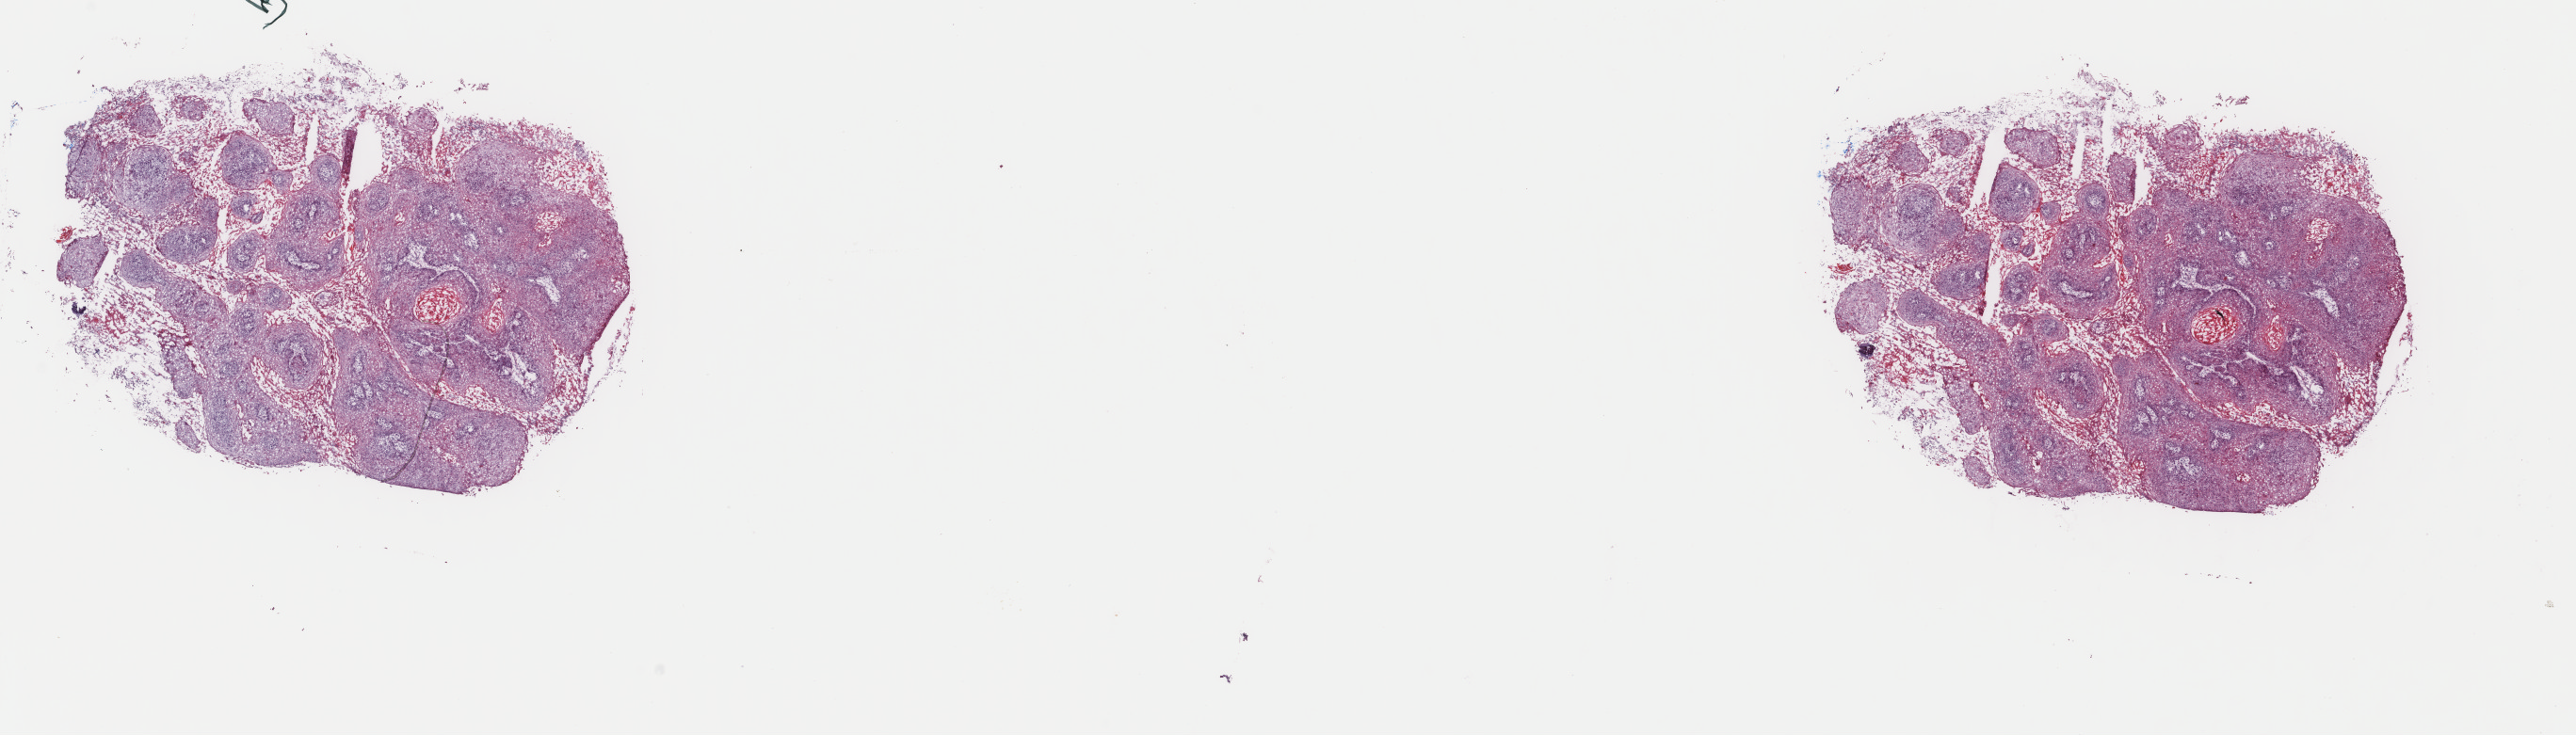
Whole-slide histology image, H&E-stained — a low-resolution overview of the entire scanned area, about 21.7 x 6.2 mm (slide scanned at 40x). Frozen section. Primary tumour sample from the head and neck. Male, age 50 years at initial diagnosis. Histologic grade: G2 (moderately differentiated). Slide review estimates, as recorded: tumour cells 100%, tumour nuclei 80%, normal cells 0%, stromal cells 0%, necrosis 0%. Infiltration values recorded for this section: lymphocyte infiltration 3%, monocyte infiltration 0%, neutrophil infiltration 0%.
• diagnosis: Squamous cell carcinoma, NOS
• TNM: T4a N0 M0
• laterality: left
• AJCC pathologic stage: IVA (7th edition)